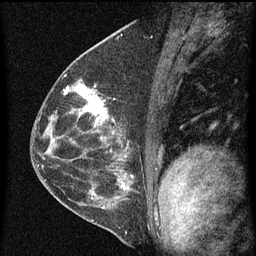
Breast MRI (dynamic contrast-enhanced), one sagittal slice. Position 33 of 60 along the scan axis. Dynamic contrast-enhanced series, image 2 of 4 at this slice position (ordered by acquisition). 1.5 T. TE 4.2 ms, TR 8 ms. 2 mm slice thickness. 256 × 256 image matrix. Female patient, age 48 years.
Structures marked on this image (semi-automatically segmented with operator editing):
- analysis volume of interest (the breast-tissue region the enhancement analysis was run in; not a lesion): bounding box [x1, y1, x2, y2] px = [73, 82, 115, 139]
- tumour enhancement mask (voxels above the 70 % enhancement threshold inside the analysis volume of interest): [78, 86, 114, 135]